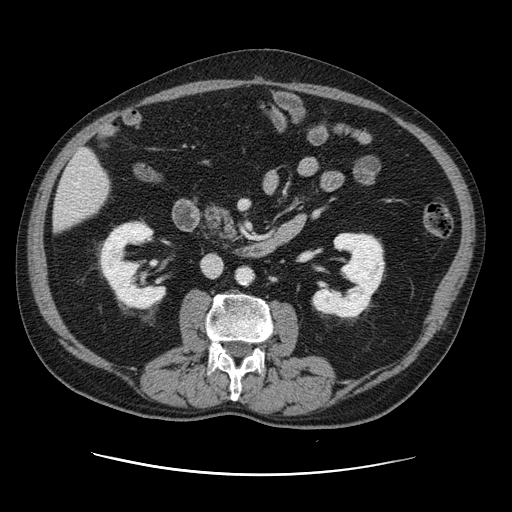
Contrast-enhanced abdominal CT, one axial slice; position 38 of 141 along the scan axis; intravenous contrast given; soft-tissue window (W 400 / L 40 HU); 2.5 mm slice thickness; 512 × 512 image matrix, field of view 395 × 395 mm. Male patient, age 72 years. From the clinical record (not read from this slice): diagnosis: colorectal cancer liver metastases, imaged before liver resection; multiple liver metastases: yes; largest metastasis: 5.4 cm.
Outlined on this slice (manually delineated by an expert):
- hepatic veins: box from (x=75, y=182) to (x=78, y=185) px
- liver: (x=54, y=150)–(x=110, y=231)
- planned liver remnant (the part of the liver to remain after resection): (x=54, y=150)–(x=110, y=231)